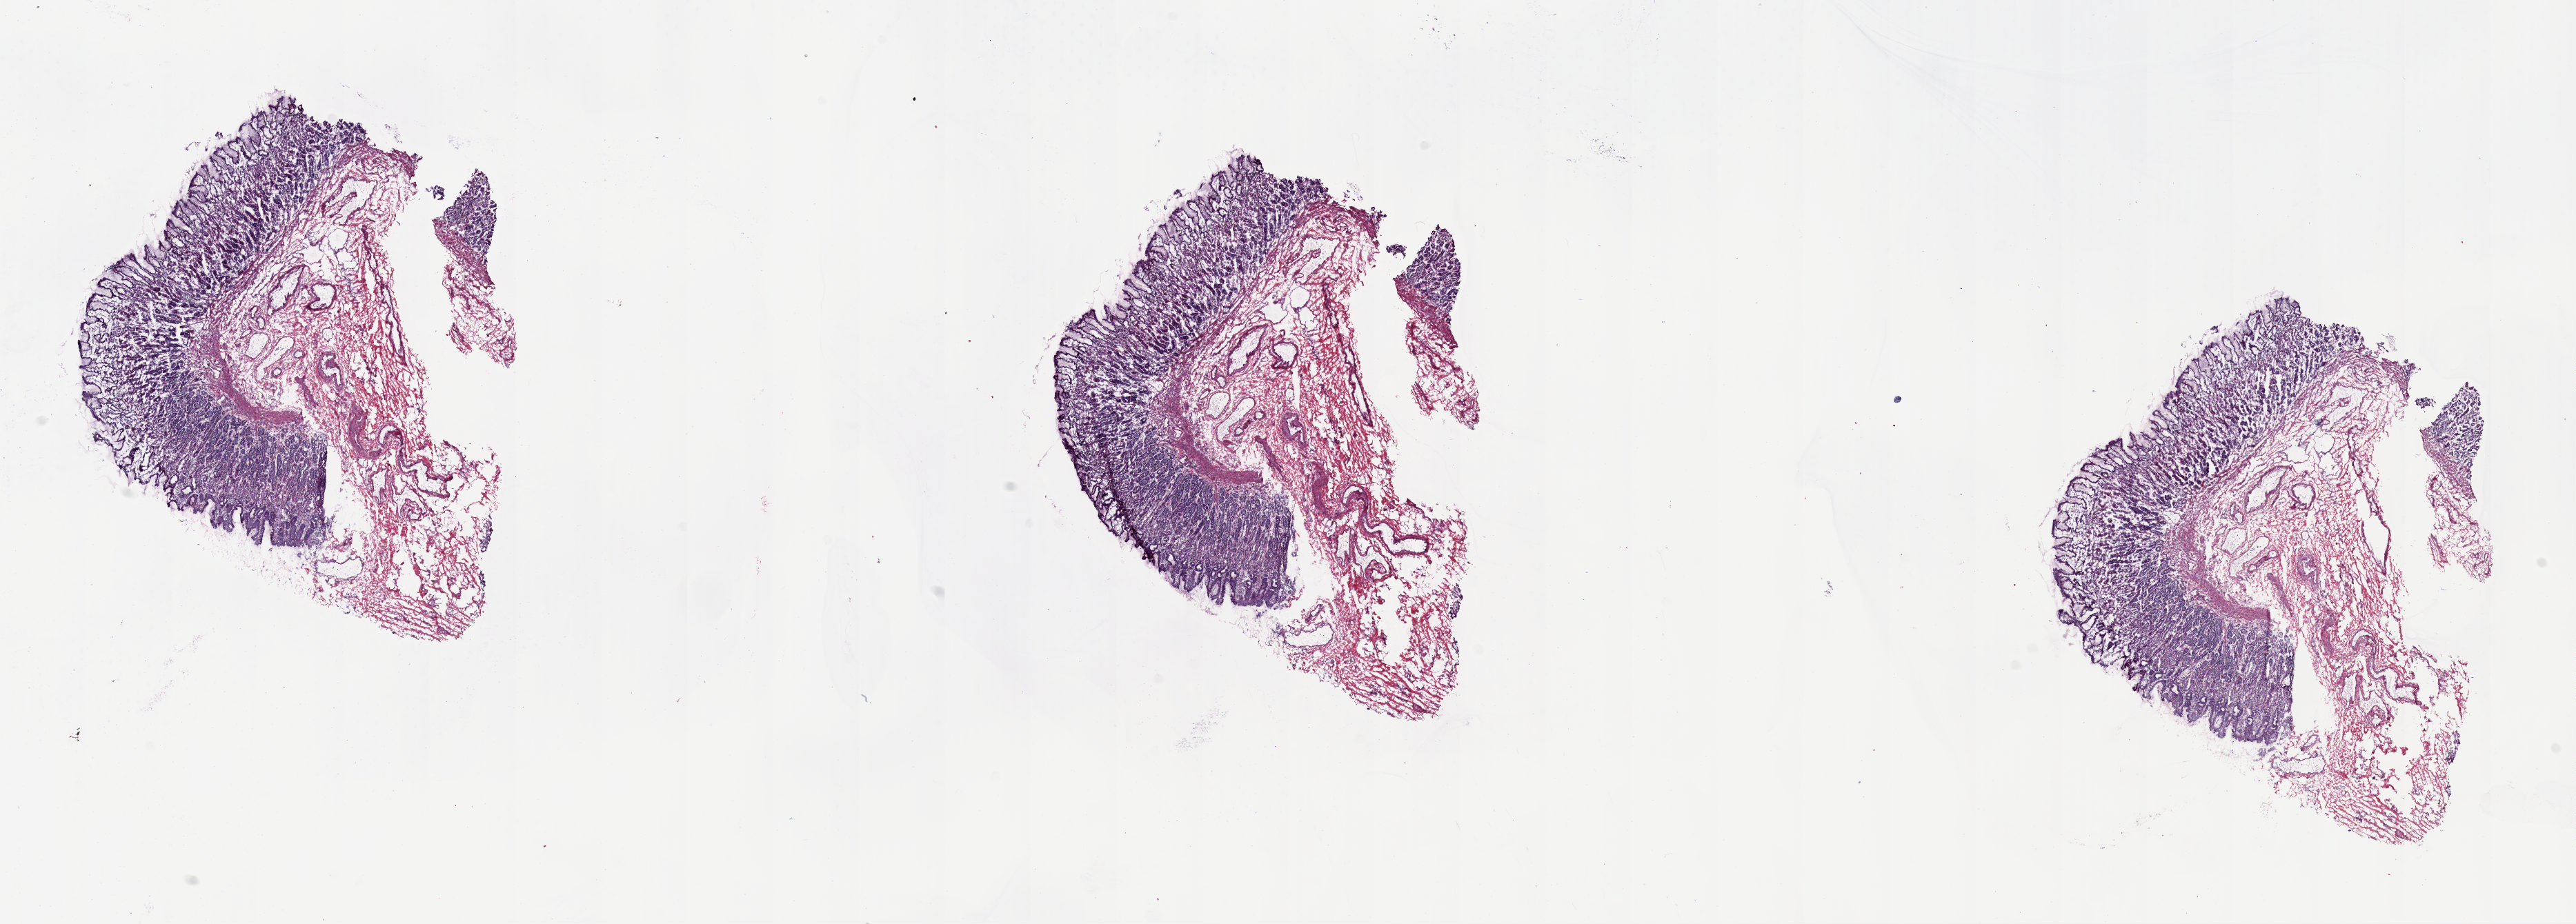
H&E-stained whole-slide image, a low-resolution overview of the entire scanned area, about 29.4 x 10.6 mm. Frozen section from the top of the tissue portion. Solid tissue normal (non-tumour tissue) sample from the esophagus. Male patient; age at initial diagnosis 79 years. Slide review estimates, as recorded: tumour cells 0%, tumour nuclei 0%, normal cells 100%, stromal cells 0%, necrosis 0%. Infiltration values recorded for this section: lymphocyte infiltration 0%, monocyte infiltration 0%, neutrophil infiltration 0%.
This section: solid tissue normal (non-tumour) sample from the same patient. Patient diagnosis: Adenocarcinoma, NOS (lower third of esophagus).